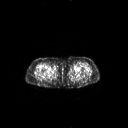
FDG PET of an extremity soft-tissue mass (from a PET/CT study), one axial slice. Slice 245 of 311 in the series (ordered by position). 3.27 mm slice thickness. 128 × 128 image matrix. Patient: female, 78 years. From the clinical record (not read from this slice): histological type: leiomyosarcoma; grade: intermediate; site of the primary tumour: parascapusular.
Annotated regions visible in this slice (expert contour drawn on MRI and transferred to this co-registered scan by the dataset authors):
- gross tumour volume including surrounding oedema: box from (x=53, y=65) to (x=58, y=69) px
- gross tumour volume (mass): (x=53, y=65)–(x=57, y=69)